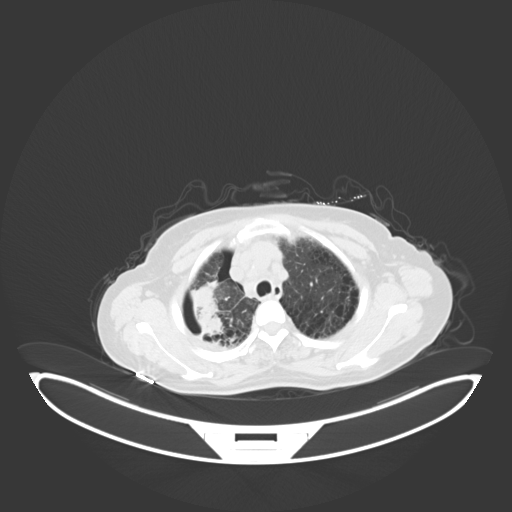
Chest CT, one axial slice; position 51 of 69 along the scan axis; lung window (W 1500 / L -600 HU); 3 mm slice thickness; 512 × 512 image matrix, field of view 500 × 500 mm. Female patient, age 64 years. Case-level facts recorded for this patient, not image findings: clinical TNM (as recorded): T3 N3 M0.
Outlined on this slice (rectangle marked by the reading radiologist):
- lung tumour (recorded histology: squamous cell carcinoma): box from (x=187, y=280) to (x=231, y=346) px